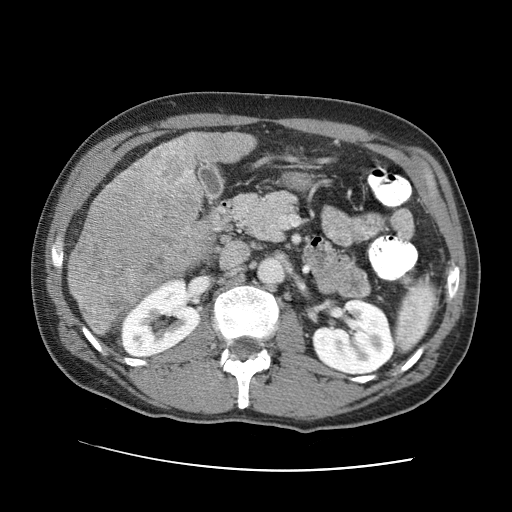
Contrast-enhanced abdominal CT (liver protocol), one axial slice. Position 31 of 95 along the scan axis. Reconstruction kernel STANDARD. One of 2 acquisitions stored at this slice position. Soft-tissue window (W 400 / L 40 HU). 512 × 512 image matrix, field of view 360 × 360 mm. From the clinical record (not read from this slice): diagnosis: hepatocellular carcinoma (patient treated with transarterial chemoembolisation; whether this scan precedes or follows treatment is not stated here); TNM stage (as recorded): Stage-IVA; Child-Pugh class: A; tumour nodularity: multinodular.
Structures marked on this image (semi-automatically segmented with operator editing):
- liver parenchyma outside the tumour (the mass and vessels are separate outlines, so this box may not span the whole liver): bounding box [x1, y1, x2, y2] px = [70, 132, 254, 255]
- mass: [67, 139, 216, 337]
- liver vessels: [179, 138, 192, 145]